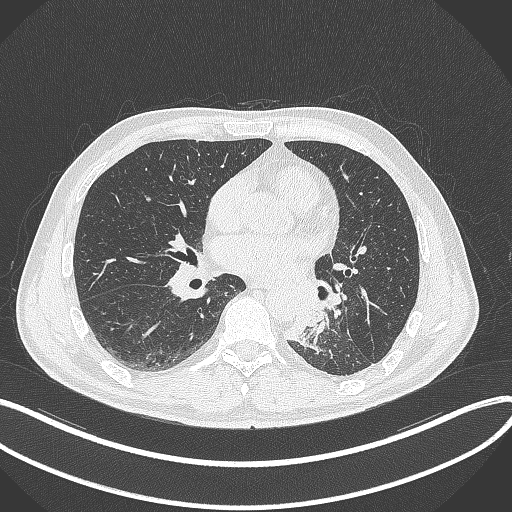
Chest CT, one axial slice; position 153 of 329 along the scan axis; reconstruction kernel B70f; 120 kVp; lung window (W 1500 / L -600 HU); 1 mm slice thickness; 512 × 512 image matrix, field of view 400 × 400 mm. Patient: male, 59 years. From the clinical record (not read from this slice): clinical TNM (as recorded): T2a N2 M0.
Annotated regions visible in this slice (bounding box drawn by a radiologist):
- lung tumour (recorded histology: squamous cell carcinoma): bounding box [x1, y1, x2, y2] px = [282, 287, 325, 344]